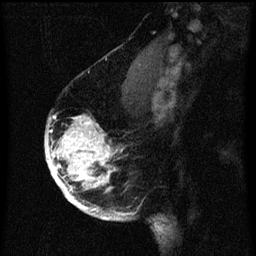
Breast MRI (dynamic contrast-enhanced), one sagittal slice; slice 44 of 60 in the series (ordered by position); dynamic contrast-enhanced series, image 2 of 3 at this slice position (ordered by acquisition); 1.5 T; TE 4.2 ms, TR 8 ms; 256 × 256 image matrix, field of view 180 × 180 mm. Patient: female, 56 years.
Annotated regions visible in this slice (semi-automatic segmentation, software-assisted and operator-edited):
- analysis volume of interest (the breast-tissue region the enhancement analysis was run in; not a lesion): bounding box (x1, y1, x2, y2) in pixels: (46, 116, 125, 219)
- tumour enhancement mask (voxels above the 70 % enhancement threshold inside the analysis volume of interest): (46, 116, 125, 219)